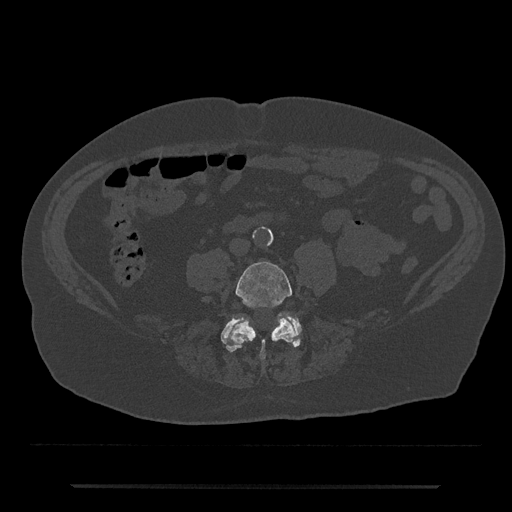
CT including the spine, one axial slice; position 333 of 797 along the scan axis; bone window (W 1800 / L 400 HU); 0.5 mm slice thickness; 512 × 512 image matrix, field of view 434 × 434 mm. Patient: male, 80 years. Case-level facts recorded for this patient, not image findings: primary cancer: prostate.
Outlined on this slice (semi-automatic segmentation, software-assisted and operator-edited):
- L4 vertebra: bounding box <226,261,296,360> (left, top, right, bottom; pixels)
- L5 vertebra: <221,314,302,352>